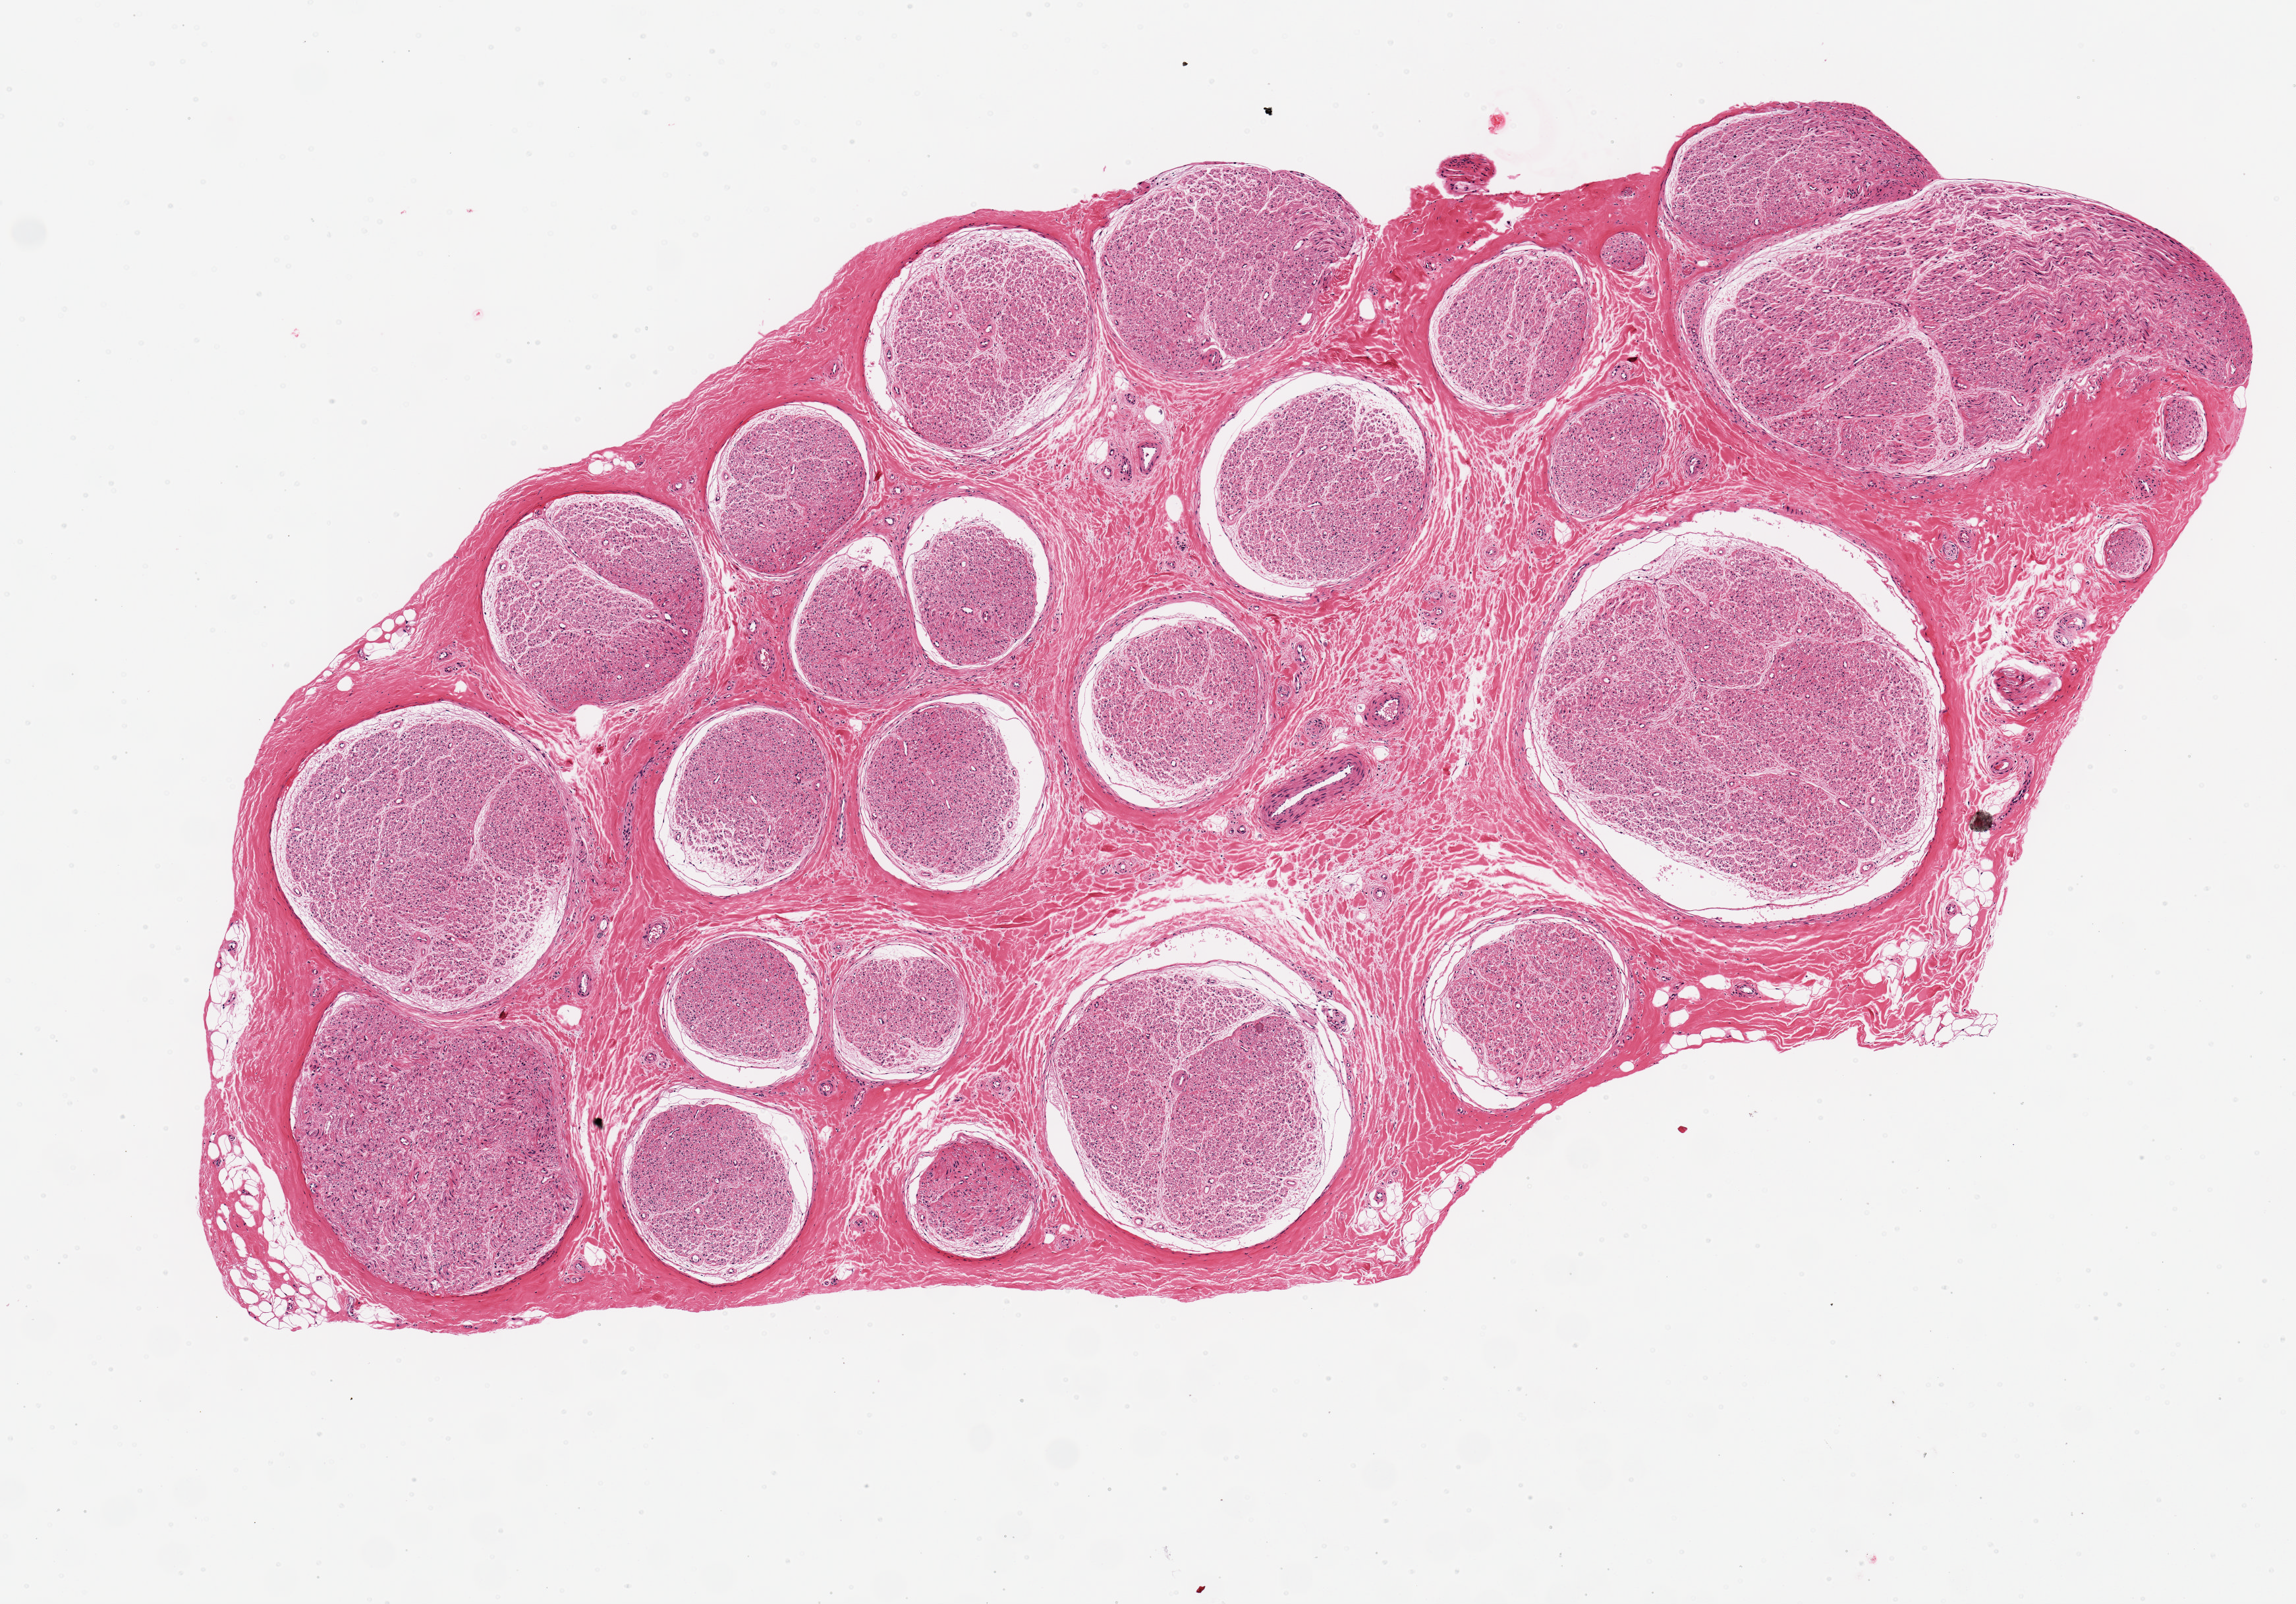
H&E whole-slide image — whole scanned area (about 6.9 x 4.8 mm, slide scanned at 20x) shown as a low-resolution overview; PAXgene-fixed, paraffin-embedded tissue; section of tibial nerve (target tissue); donor tissue sample. Male donor.
Review note (as recorded): 3.3x 6.7 ~40% intermingled fibroconnective tissue.